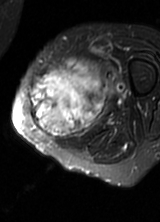
MRI of an extremity soft-tissue mass, one axial slice; position 23 of 69 along the scan axis; T2-weighted fat-saturated; MR volume resampled by the dataset authors to the PET/CT grid (not the native acquisition matrix); 3.27 mm slice thickness; 160 × 222 image matrix, field of view 156 × 217 mm. Female patient. Case-level facts recorded for this patient, not image findings: histological type: pleomorphic leiomyosarcoma; grade: high; site of the primary tumour: left thigh.
Structures marked on this image (expert contour drawn on MRI and transferred to this co-registered scan by the dataset authors):
- gross tumour volume including surrounding oedema: bounding box <29,59,112,140> (left, top, right, bottom; pixels)
- gross tumour volume (mass): <29,72,106,139>